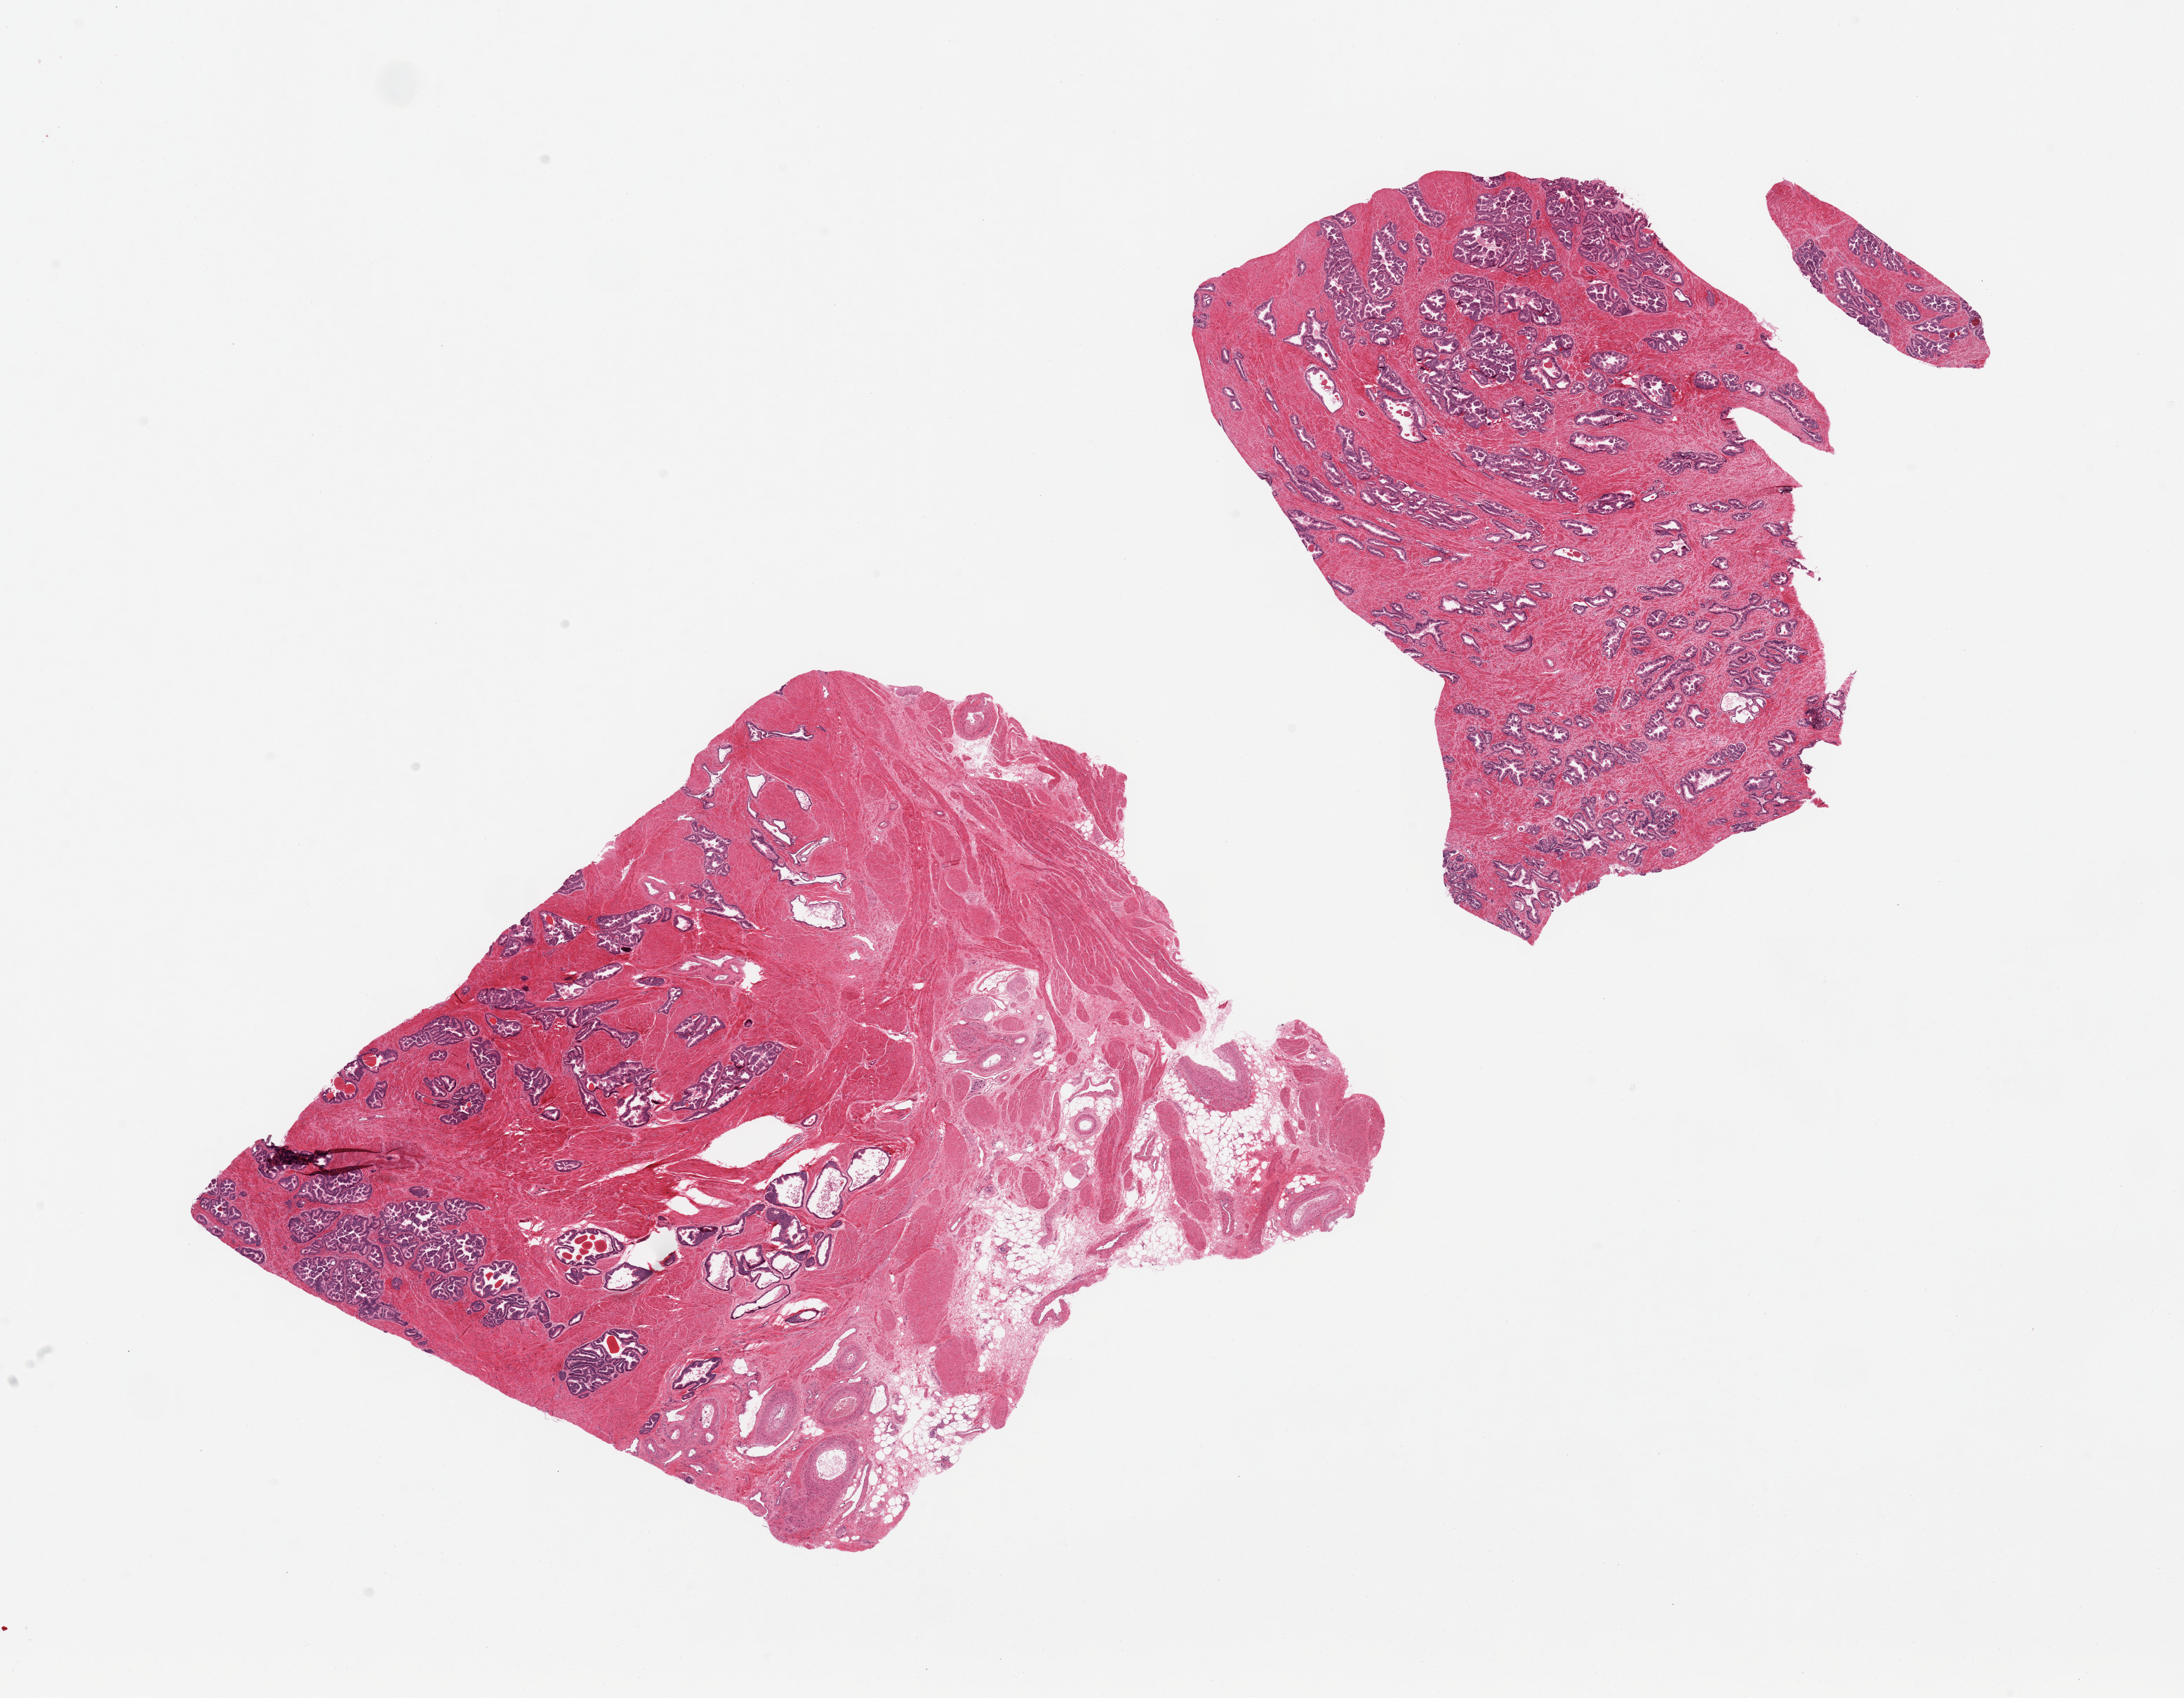
Digitized H&E-stained section, brightfield — a low-resolution overview of the entire scanned area, about 24.6 x 19.1 mm; PAXgene-fixed, paraffin-embedded tissue; target tissue: prostate; donor tissue sample. Male donor.
Review note (as recorded): 2 pieces, hyperplastic glandular pattern, adherent fat/fibrous tissue on section.